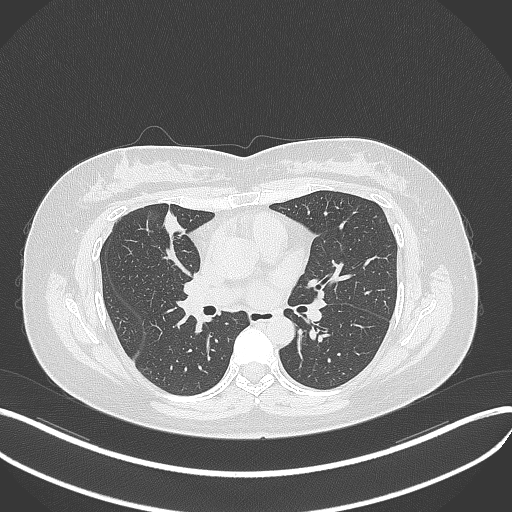
Chest CT, one axial slice. Position 168 of 273 along the scan axis. 120 kVp. Lung window (W 1500 / L -600 HU). 1 mm slice thickness. 512 × 512 image matrix, field of view 400 × 400 mm. Female patient, age 42 years. From the clinical record (not read from this slice): clinical TNM (as recorded): T1b N0 M0.
Outlined on this slice (rectangle marked by the reading radiologist):
- lung tumour (recorded histology: adenocarcinoma): bounding box (x1, y1, x2, y2) in pixels: (162, 201, 187, 243)